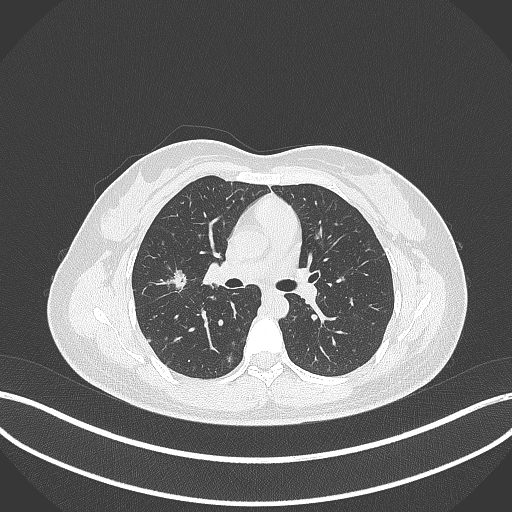
Chest CT, one axial slice; position 197 of 307 along the scan axis; reconstruction kernel B70f; 120 kVp; lung window (W 1500 / L -600 HU); 512 × 512 image matrix, field of view 400 × 400 mm. Patient: female, 33 years. Case-level facts recorded for this patient, not image findings: clinical TNM (as recorded): T1c N0 M0; histopathological grade: G2-G3.
Structures marked on this image (rectangle marked by the reading radiologist):
- lung tumour (recorded histology: adenocarcinoma): bounding box <168,266,189,294> (left, top, right, bottom; pixels)